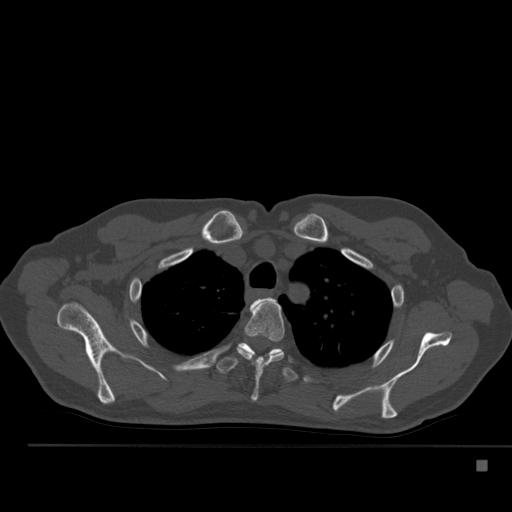
CT including the spine, one axial slice. Position 393 of 517 along the scan axis. 120 kVp. Bone window (W 1800 / L 400 HU). 1.5 mm slice thickness. 512 × 512 image matrix, field of view 408 × 408 mm. Patient: male, 70 years. From the clinical record (not read from this slice): primary cancer: renal; vertebrae with lytic lesions (as recorded): T4, T6, T10, T12, L3, L4, L5.
Annotated regions visible in this slice (semi-automatic segmentation, software-assisted and operator-edited):
- T2 vertebra: box from (x=253, y=298) to (x=275, y=306) px
- T3 vertebra: (x=237, y=300)–(x=285, y=401)
- T4 vertebra: (x=216, y=343)–(x=299, y=381)